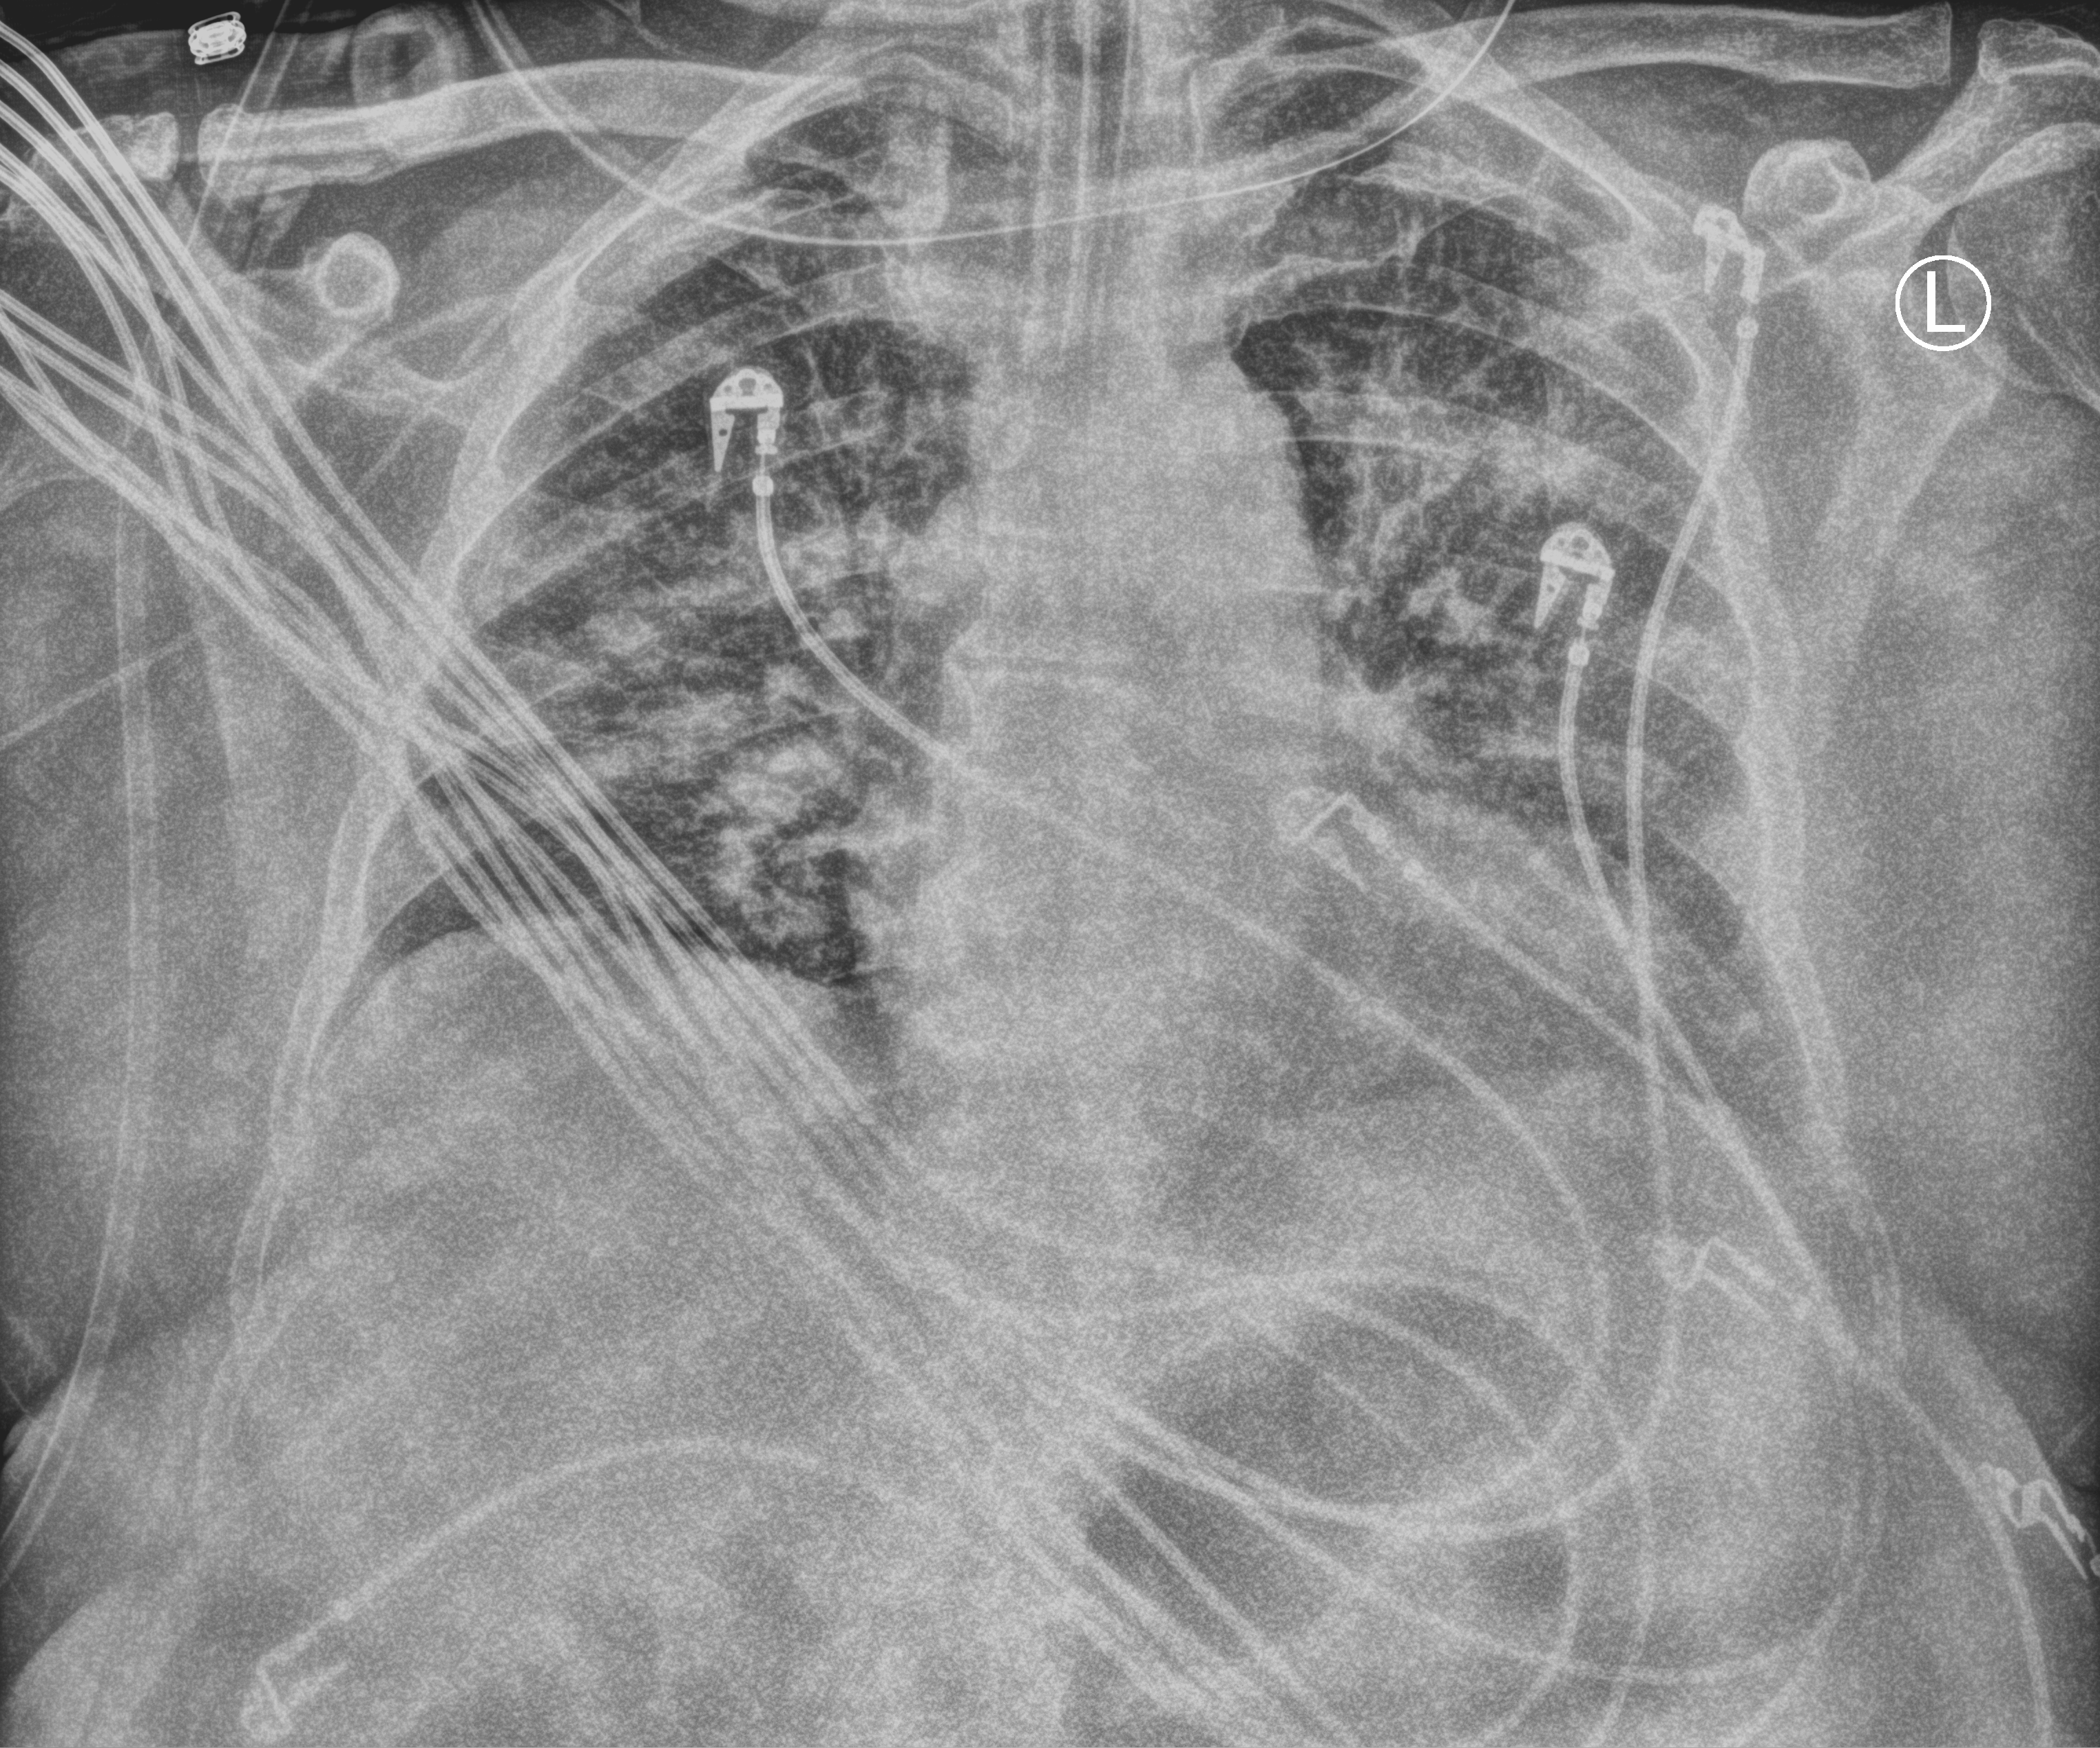
Portable chest radiograph; anteroposterior (AP) projection. Patient hospitalised with COVID-19; male, aged 60–74 years.
Admission-level facts for this patient (not findings on this image; timing relative to this image not recorded): admitted to intensive care during this hospital stay: yes; mechanically ventilated during this hospital stay: yes.